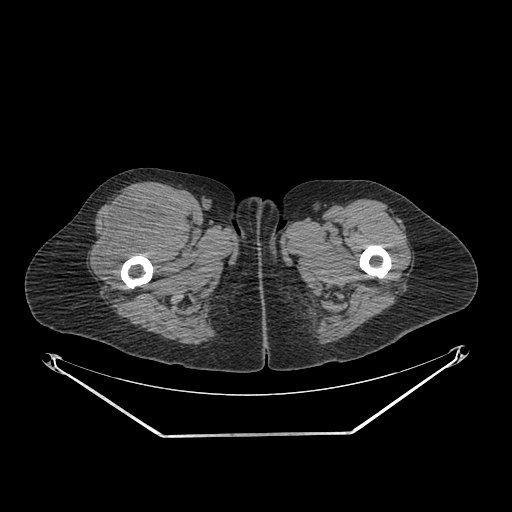
CT of an extremity soft-tissue mass (from a PET/CT study), one axial slice; slice 271 of 311 in the series (ordered by position); reconstruction kernel SOFT; 140 kVp; soft-tissue window (W 400 / L 40 HU); 512 × 512 image matrix. Female patient. Case-level facts recorded for this patient, not image findings: histological type: pleiomorphic undifferentiated sarcoma; grade: high; site of the primary tumour: right quadricep.
Annotated regions visible in this slice (expert contour drawn on MRI and transferred to this co-registered scan by the dataset authors):
- tumour plus oedema (research contour): bounding box (x1, y1, x2, y2) in pixels: (96, 190, 179, 273)
- tumour (research contour): (96, 190, 179, 273)